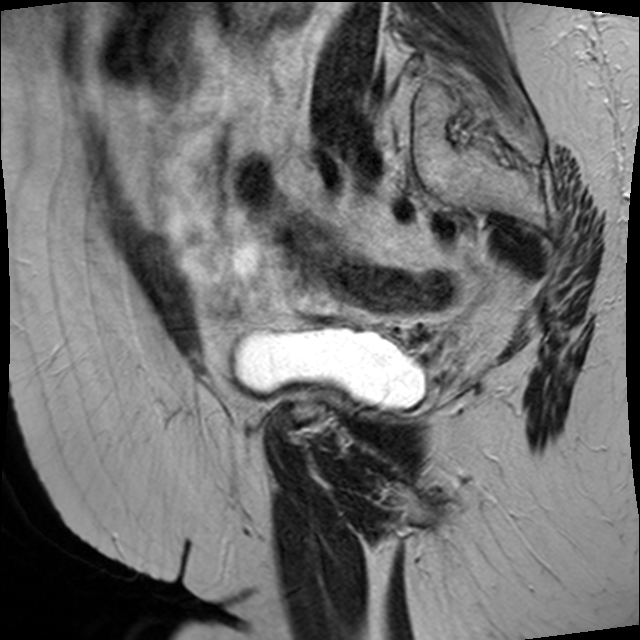
Pelvic MRI for cervical cancer, one sagittal slice; slice 31 of 45 in the series (ordered by position); T2-weighted; 1.5 T; TE 89 ms, TR 4610 ms; 640 × 640 image matrix. Patient: female, 50 years.
Annotated regions visible in this slice (outlined manually by an expert reader):
- uterus and cervix: bounding box (x1, y1, x2, y2) in pixels: (266, 202, 359, 291)